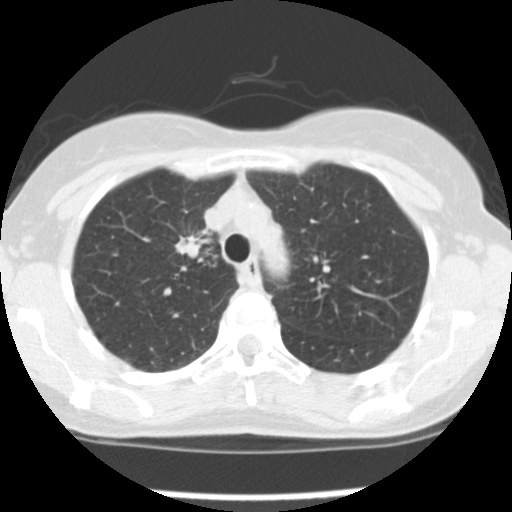
Low-dose screening chest CT, one axial slice. Reconstruction kernel STANDARD. Lung window (W 1500 / L -600 HU). 2.5 mm slice thickness. 512 × 512 image matrix, field of view 282 × 282 mm.
Outlined on this slice (manually delineated by an expert):
- lesion 1 (tumor, upper lobe of right lung): bounding box (x1, y1, x2, y2) in pixels: (175, 236, 211, 258)